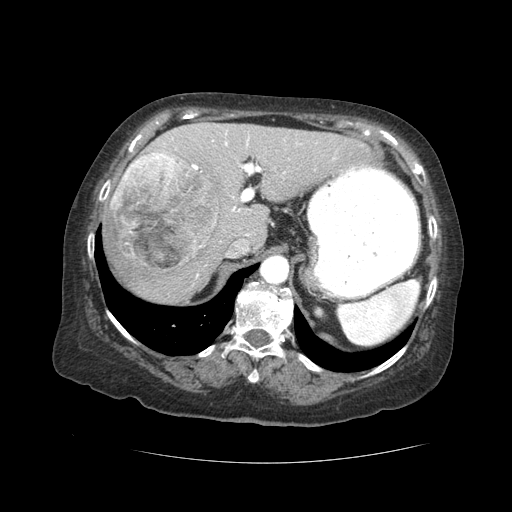
Contrast-enhanced abdominal CT (liver protocol), one axial slice. Slice 29 of 59 in the series (ordered by position). Soft-tissue window (W 400 / L 40 HU). 512 × 512 image matrix, field of view 380 × 380 mm. Case-level facts recorded for this patient, not image findings: diagnosis: hepatocellular carcinoma (patient treated with transarterial chemoembolisation; whether this scan precedes or follows treatment is not stated here); TNM stage (as recorded): Stage-I; Child-Pugh class: A.
Structures marked on this image (semi-automatic segmentation, software-assisted and operator-edited):
- liver parenchyma outside the tumour (the mass and vessels are separate outlines, so this box may not span the whole liver): box from (x=104, y=122) to (x=370, y=302) px
- mass: (x=112, y=154)–(x=218, y=271)
- liver vessels: (x=164, y=132)–(x=335, y=277)